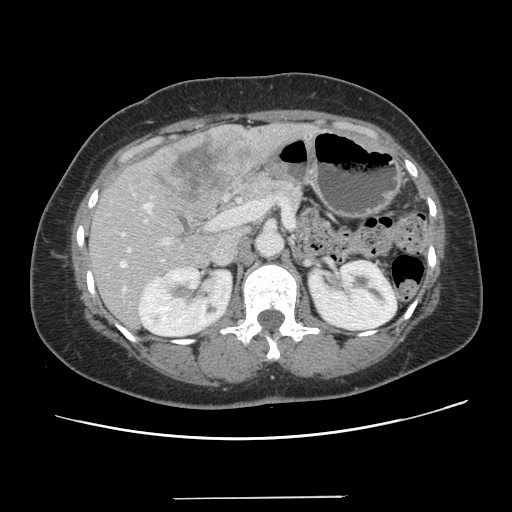
Contrast-enhanced abdominal CT, one axial slice. Position 67 of 141 along the scan axis. 120 kVp. Intravenous contrast given. Soft-tissue window (W 400 / L 40 HU). 512 × 512 image matrix, field of view 366 × 366 mm. Female patient, age 53 years. Case-level facts recorded for this patient, not image findings: diagnosis: colorectal cancer liver metastases, imaged before liver resection; multiple liver metastases: no; largest metastasis: 14.5 cm; chemotherapy before resection: yes.
Annotated regions visible in this slice (expert manual segmentation):
- hepatic veins: bounding box (x1, y1, x2, y2) in pixels: (120, 248, 129, 291)
- liver: (90, 124, 306, 328)
- planned liver remnant (the part of the liver to remain after resection): (90, 210, 247, 329)
- portal vein (with intrahepatic branches): (122, 204, 169, 244)
- liver metastasis: (152, 133, 256, 202)